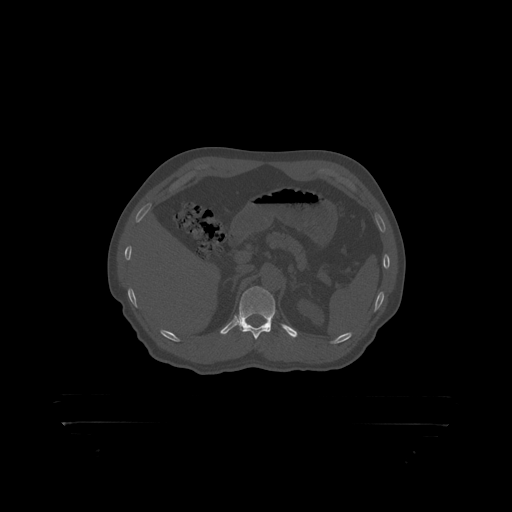
CT including the spine, one axial slice; reconstruction kernel STANDARD; 120 kVp; bone window (W 1800 / L 400 HU); 512 × 512 image matrix, field of view 650 × 650 mm. Patient: male, 46 years. From the clinical record (not read from this slice): primary cancer: skin.
Annotated regions visible in this slice (semi-automatic segmentation, software-assisted and operator-edited):
- T12 vertebra: bounding box [x1, y1, x2, y2] px = [239, 287, 276, 319]